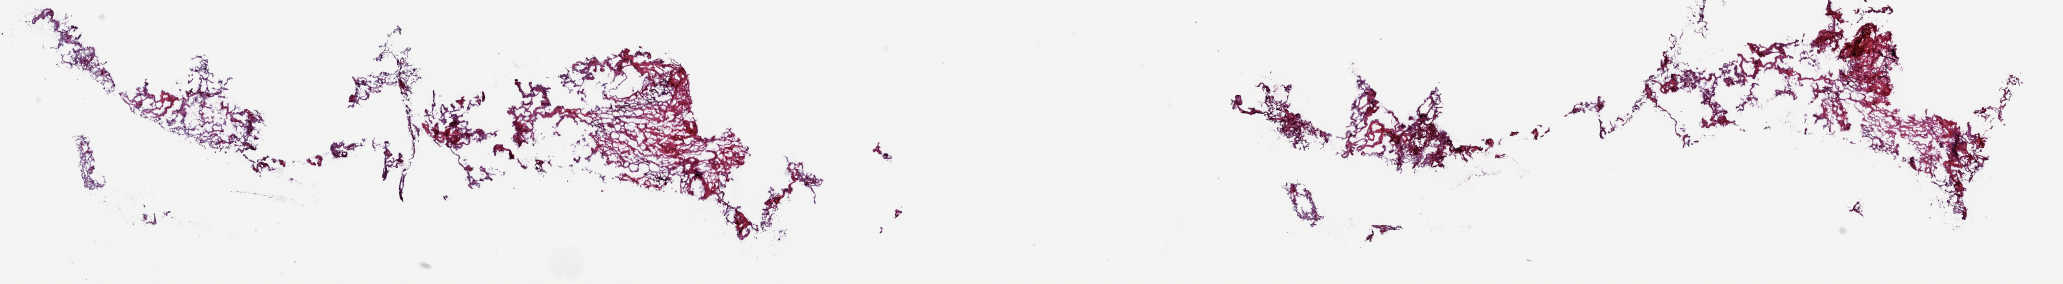
Hematoxylin and eosin (H&E) stained whole-slide image, shown as a low-resolution overview of the whole scanned area (about 32.7 x 4.5 mm); frozen section; lung, solid tissue normal (non-tumour tissue) sample. Female, age 51 years at initial diagnosis. Pathologist review of this section (percent, as recorded): tumour cells 0%, tumour nuclei 0%, normal cells 100%, stromal cells 0%, necrosis 0%. Inflammatory infiltration, as recorded: lymphocyte infiltration 0%, monocyte infiltration 0%, neutrophil infiltration 0%.
- this section: solid tissue normal sample (biorepository sample class)
- patient diagnosis: Adenocarcinoma, NOS (upper lobe, lung)